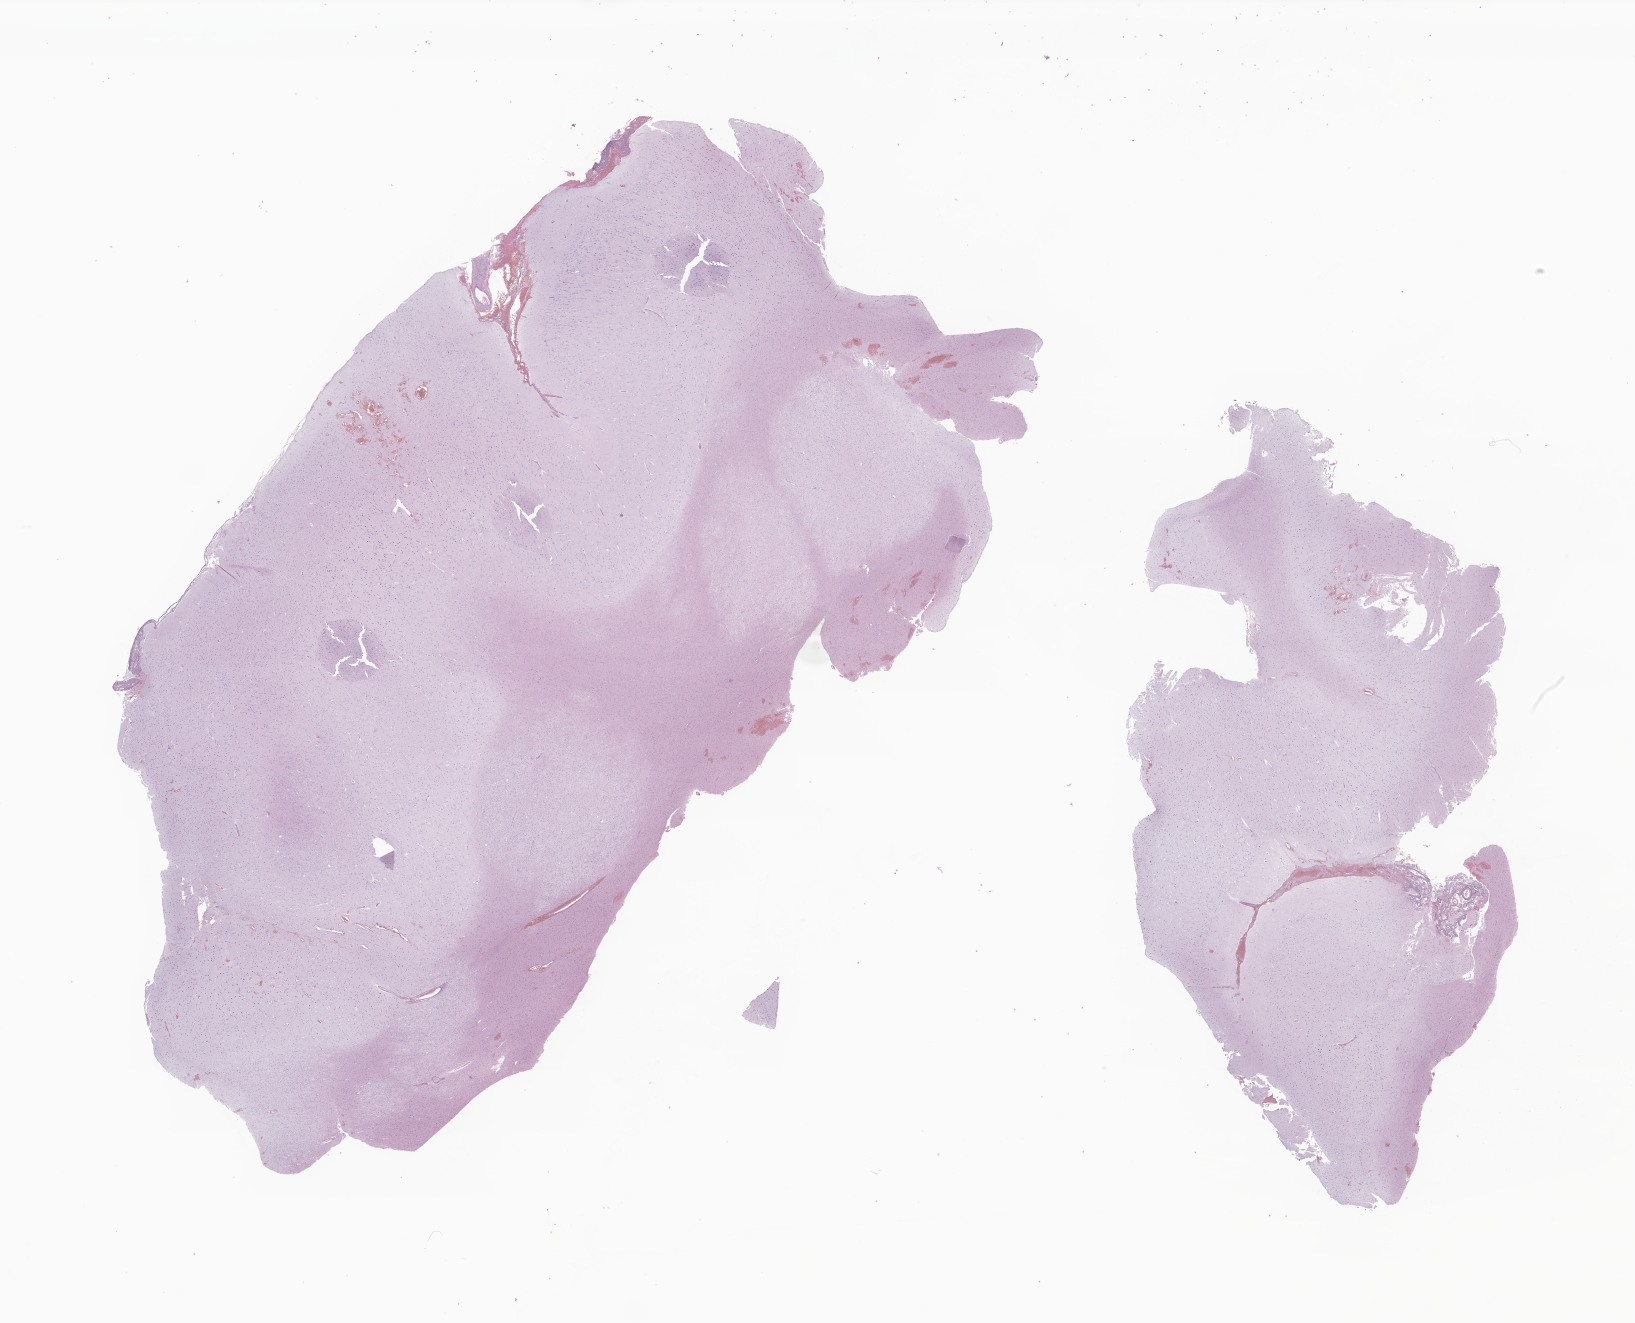
Whole-slide image, H&E stain of tumor tissue from the frontal lobe — shown as a low-resolution overview of the whole scanned area (about 27.6 x 22.3 mm), FFPE section. Male patient, age 68 months (5 years 8 months).
* recorded diagnosis: Neoplasm, uncertain whether benign or malignant